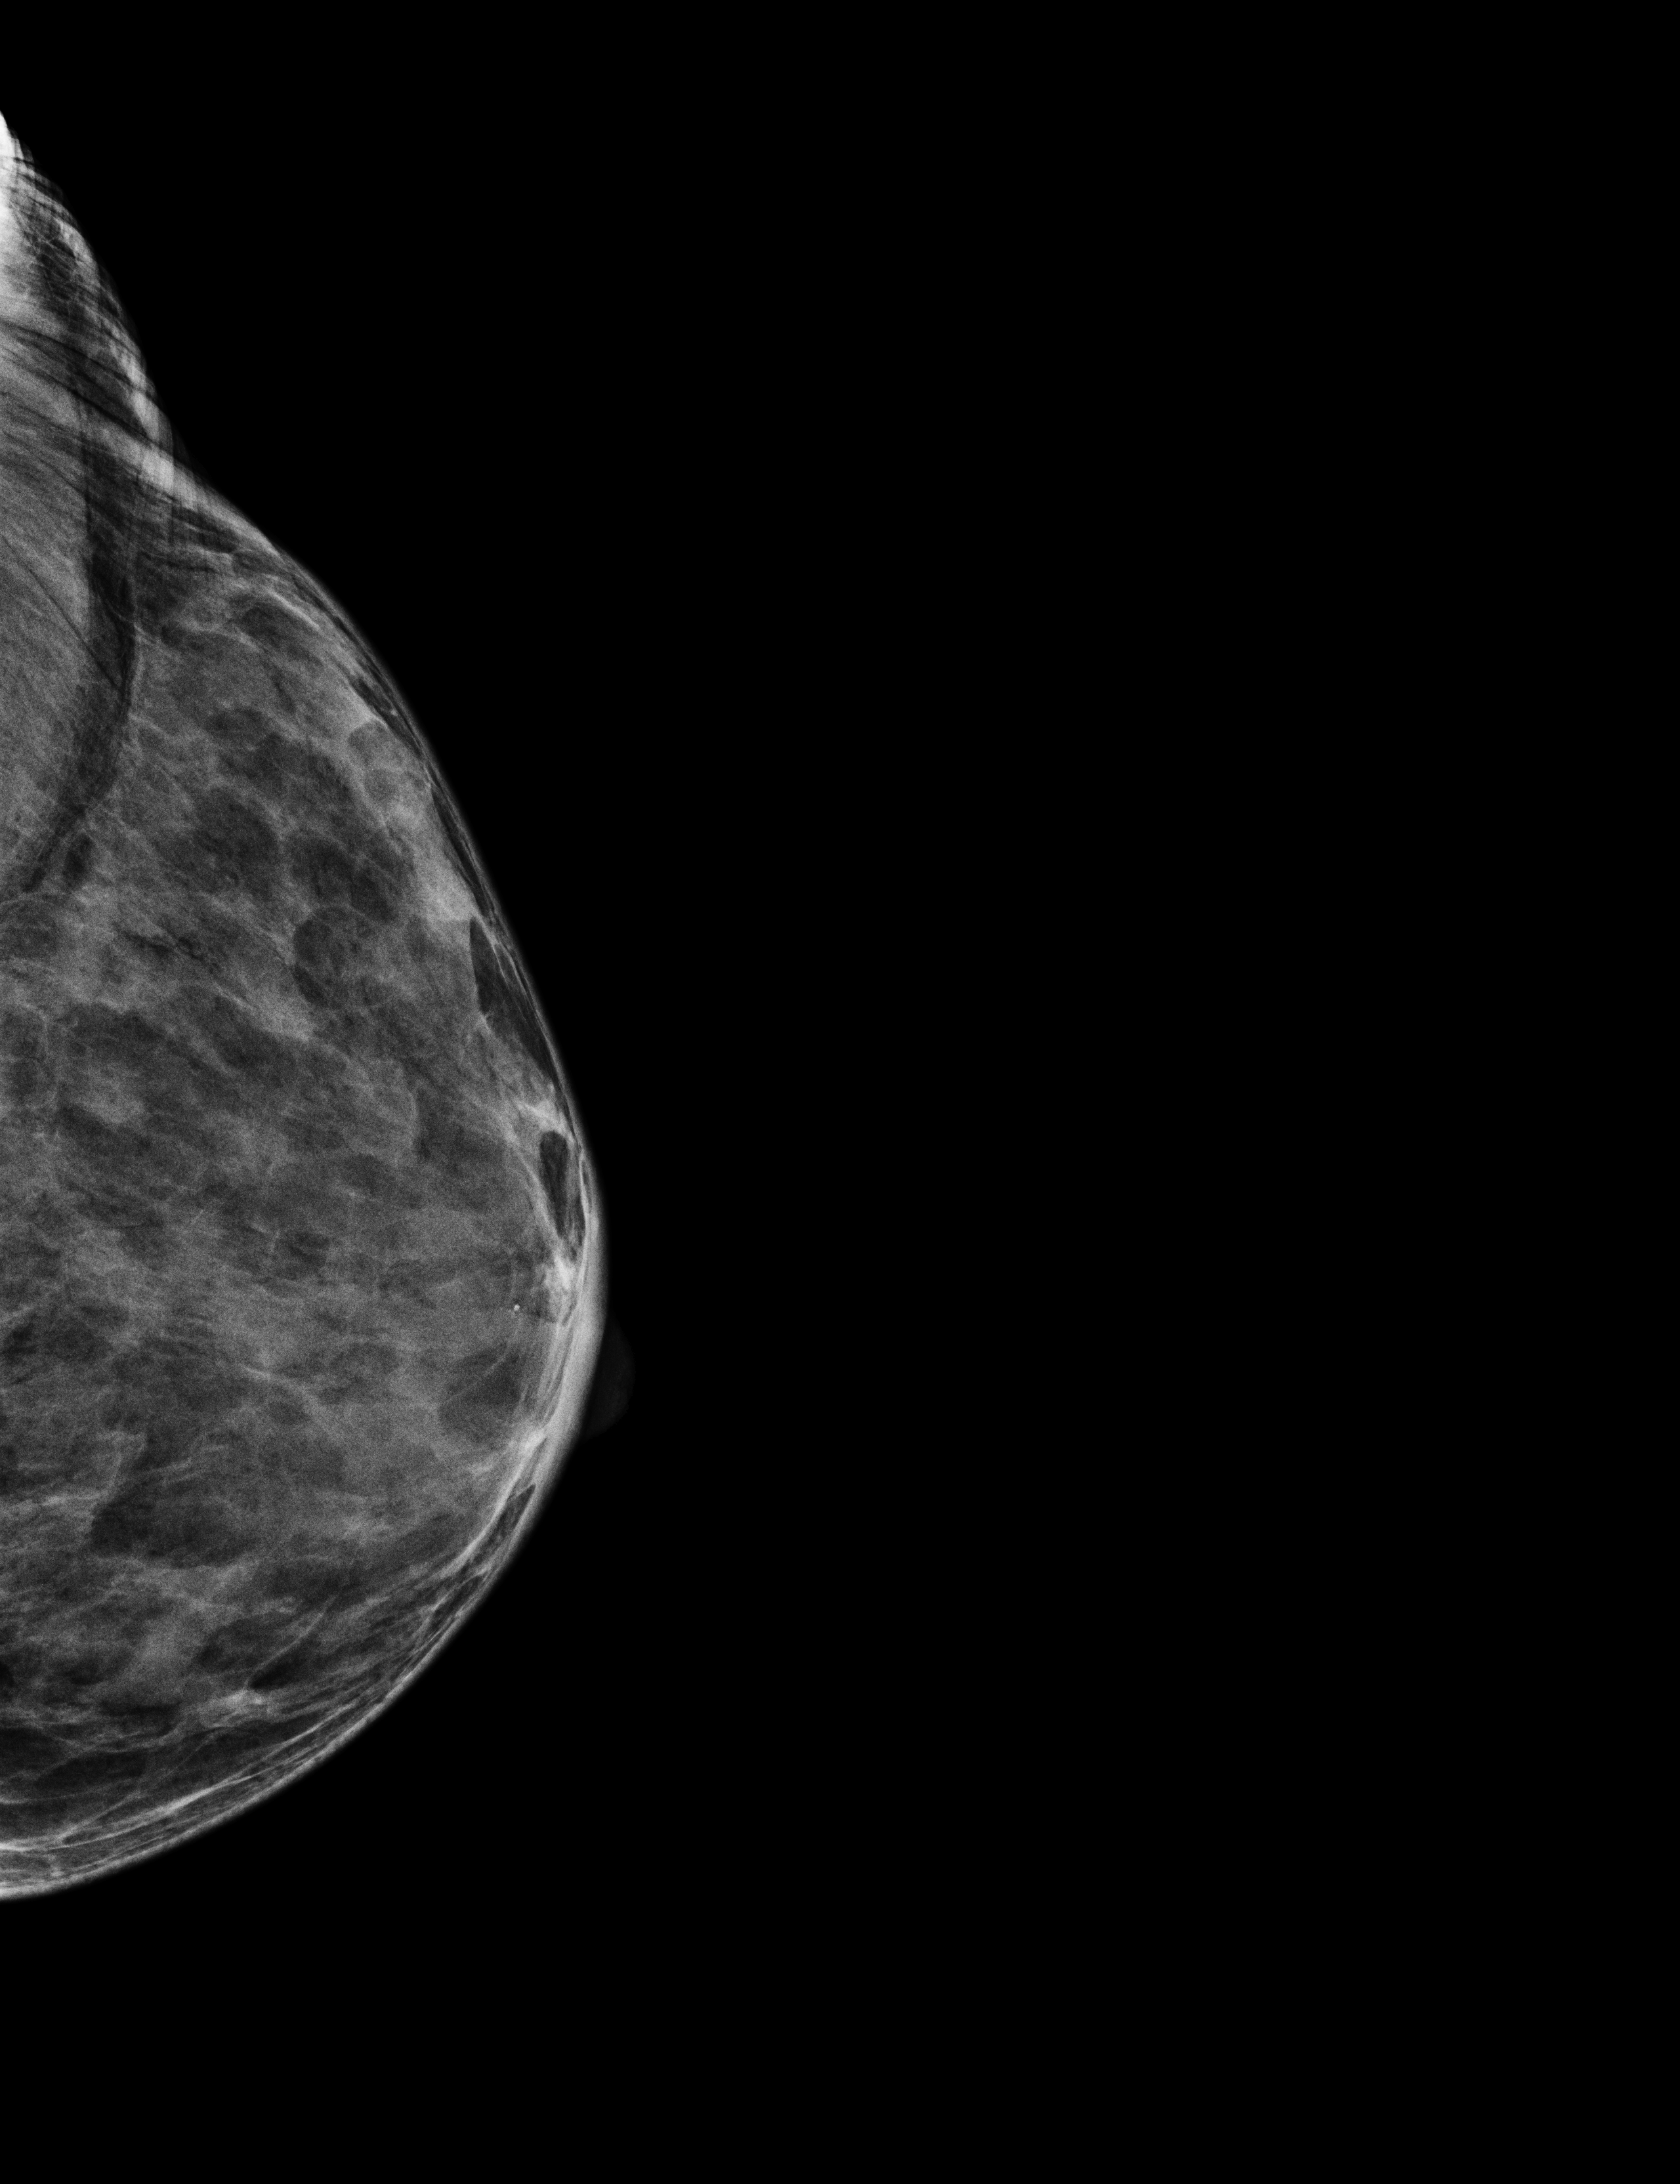
Screening examination; compressed breast thickness 19 mm; system: Selenia Dimensions. Female patient, age 69 years.
Image type: full-field digital mammogram. Breast: left. Projection: exaggerated CC view (lateral).